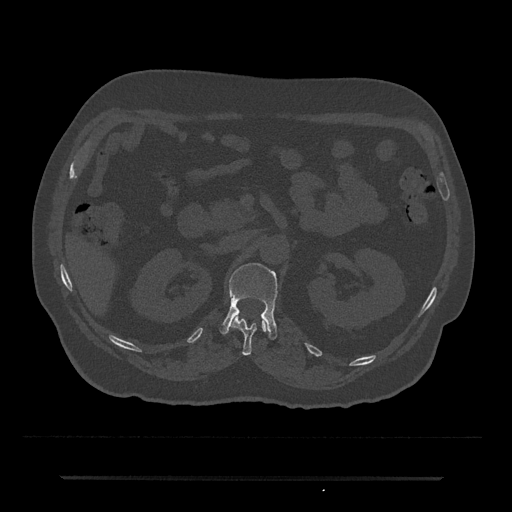
CT including the spine, one axial slice; position 93 of 797 along the scan axis; reconstruction kernel Br40s/3; 120 kVp; bone window (W 1800 / L 400 HU); 0.5 mm slice thickness; 512 × 512 image matrix. Male patient, age 69 years. From the clinical record (not read from this slice): primary cancer: prostate.
Annotated regions visible in this slice (semi-automatic segmentation, software-assisted and operator-edited):
- L1 vertebra: bounding box <219,263,278,340> (left, top, right, bottom; pixels)
- T12 vertebra: <231,314,268,355>